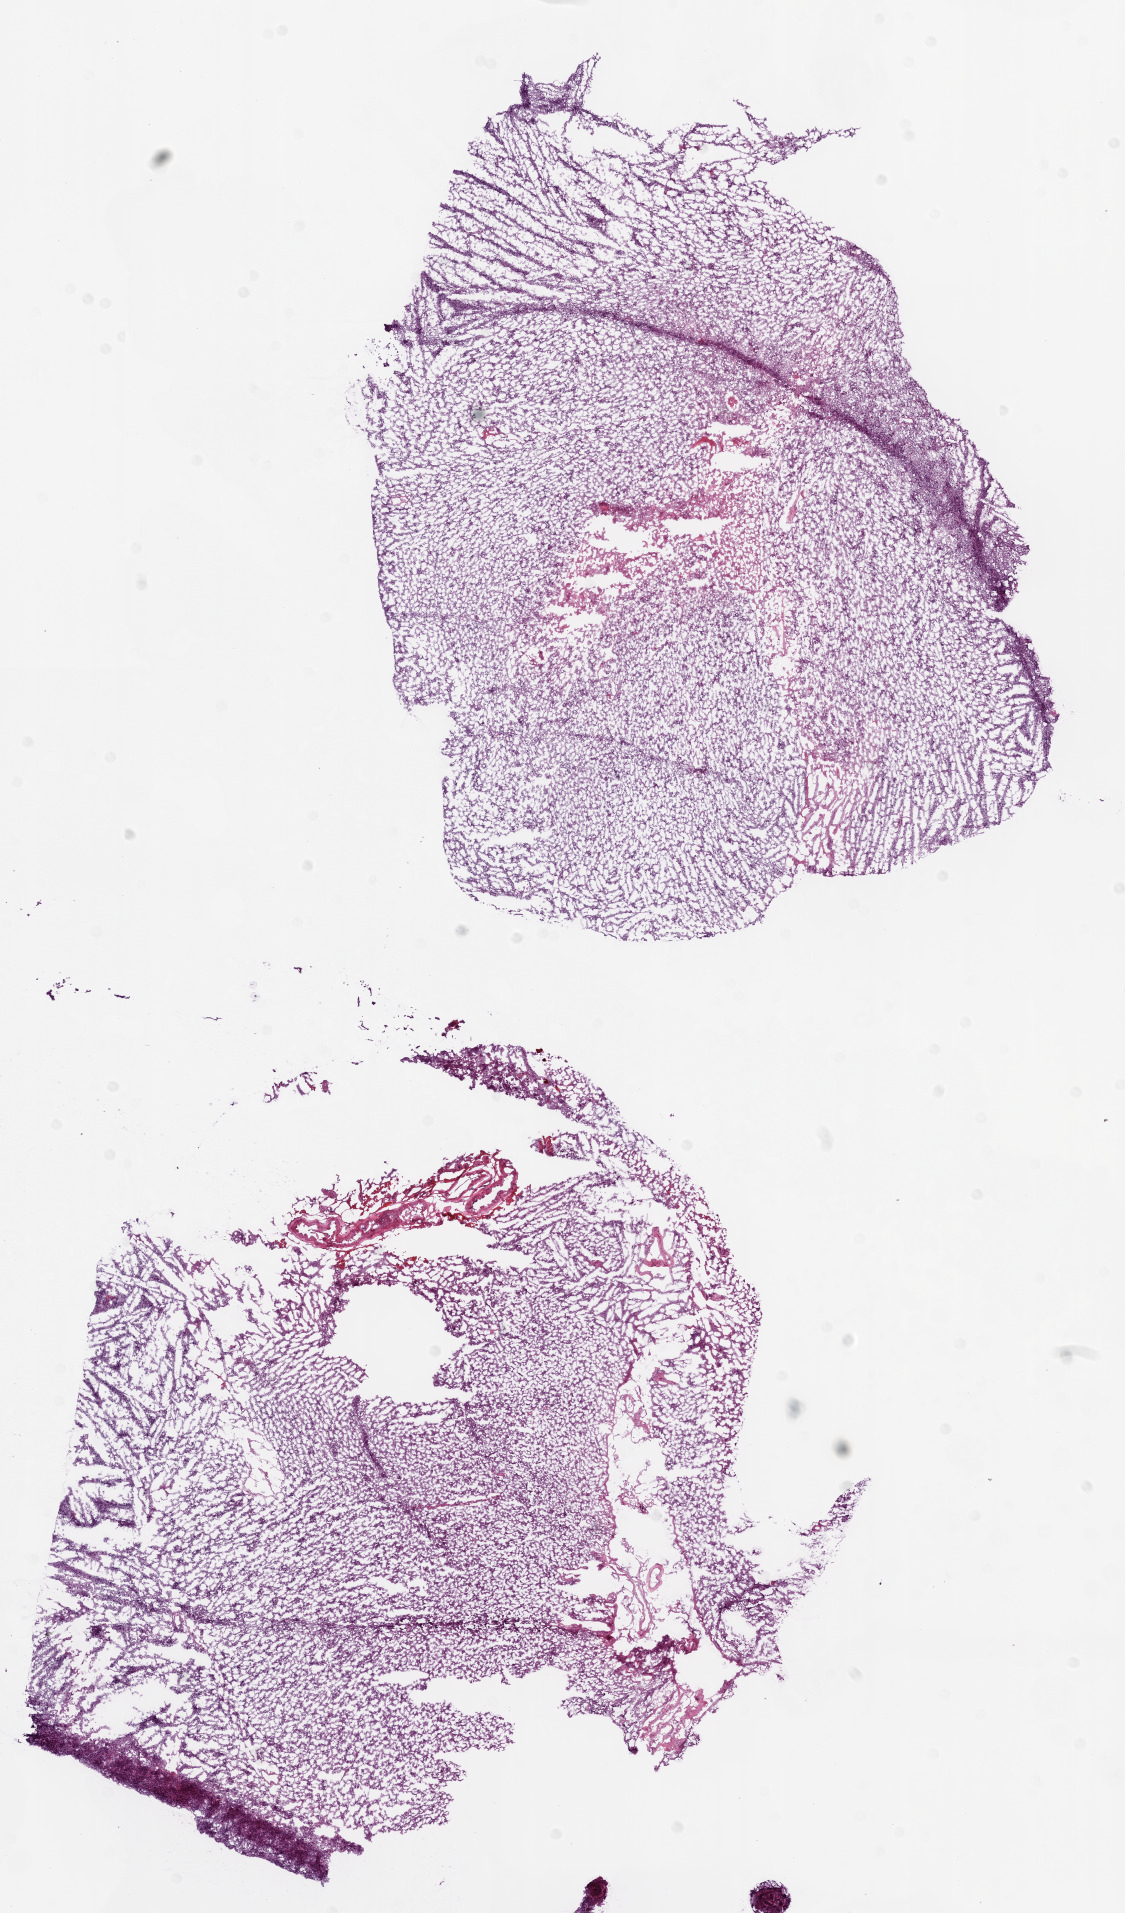
Digitized H&E tissue section (whole slide), shown as a low-resolution overview of the whole scanned area (about 9.0 x 15.3 mm, from a 20x scan), frozen section from the bottom of the tissue portion, primary tumour sample from the brain. Male patient; age at initial diagnosis 68 years. Pathologist review of this section (percent, as recorded): tumour cells 80%, tumour nuclei 90%, normal cells 10%, stromal cells 5%, necrosis 5%.
* diagnosis: Glioblastoma